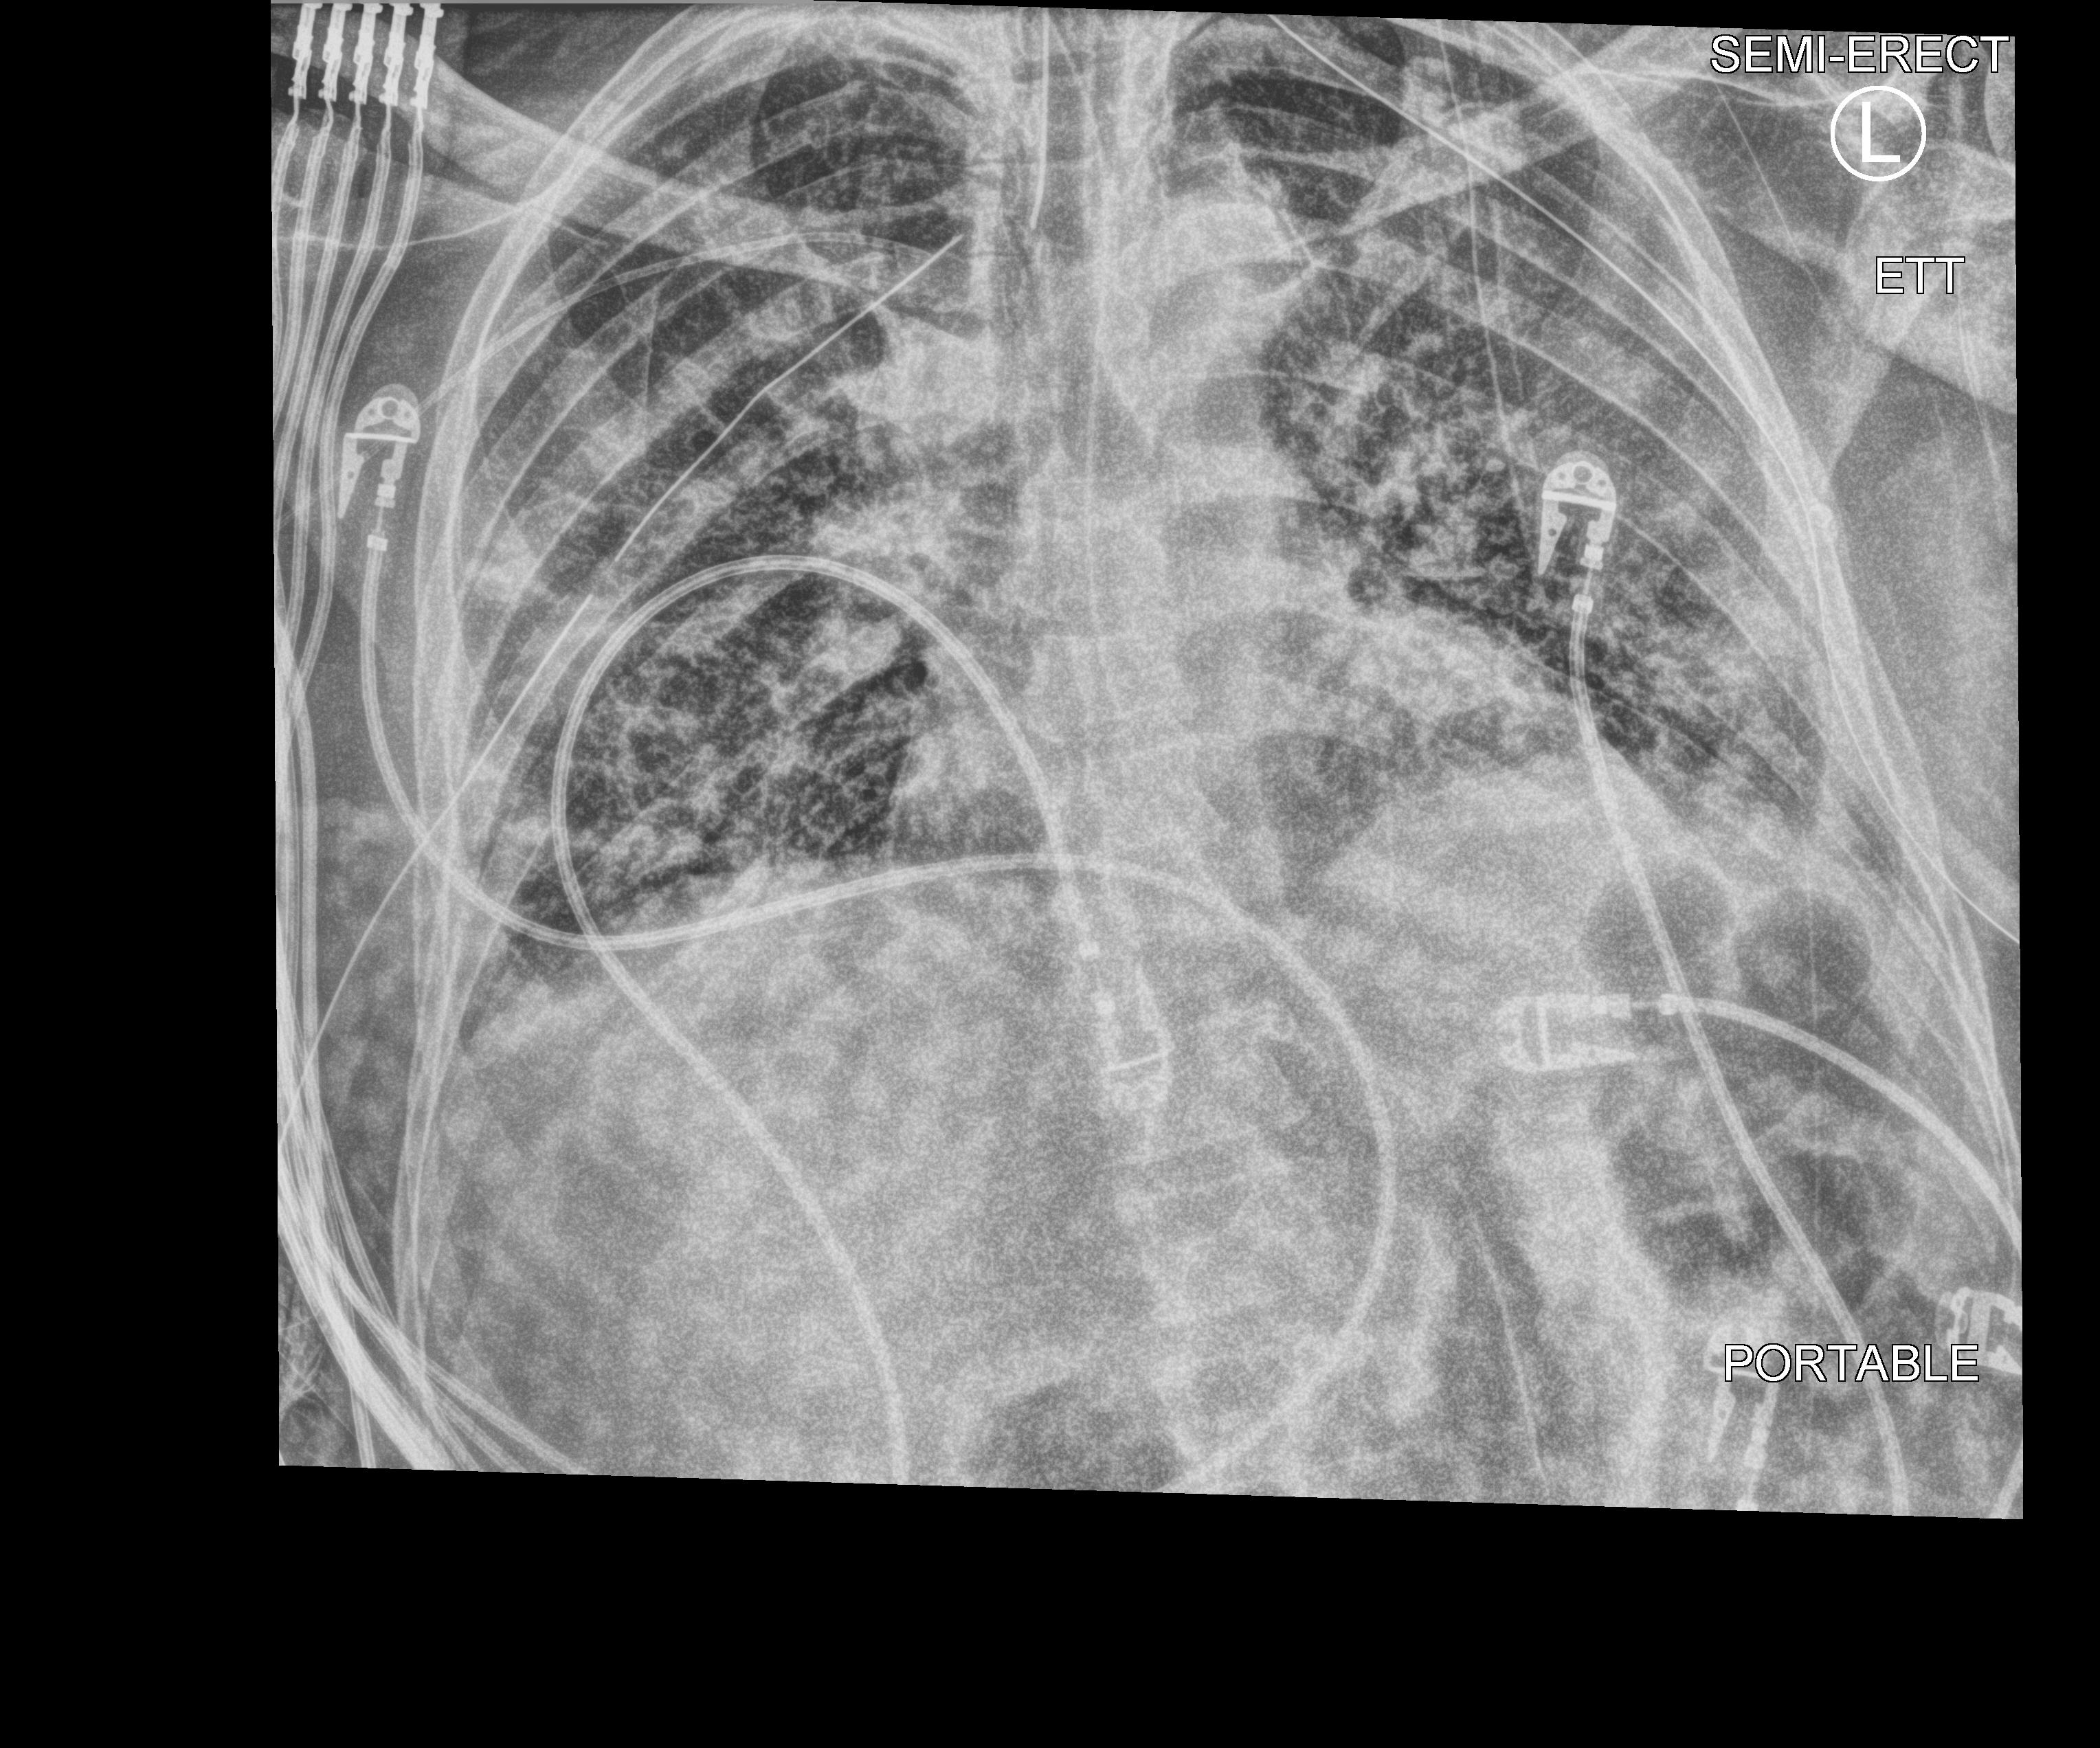
Bedside chest radiograph (computed radiography), anteroposterior (AP) projection. Patient hospitalised with COVID-19; male, aged 18–59 years.
Admission-level facts for this patient (not findings on this image; timing relative to this image not recorded): mechanically ventilated during this hospital stay: yes.